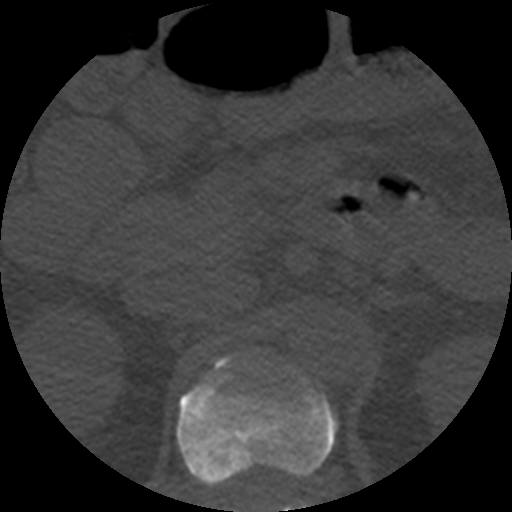
CT including the spine, one axial slice. Slice 204 of 508 in the series (ordered by position). Reconstruction kernel STANDARD. 120 kVp. Bone window (W 1800 / L 400 HU). 512 × 512 image matrix, field of view 160 × 160 mm. Patient age 57 years. Case-level facts recorded for this patient, not image findings: primary cancer: prostate.
Annotated regions visible in this slice (semi-automatic segmentation, software-assisted and operator-edited):
- L1 vertebra: bounding box (x1, y1, x2, y2) in pixels: (296, 503, 308, 512)
- T12 vertebra: (177, 356, 337, 512)